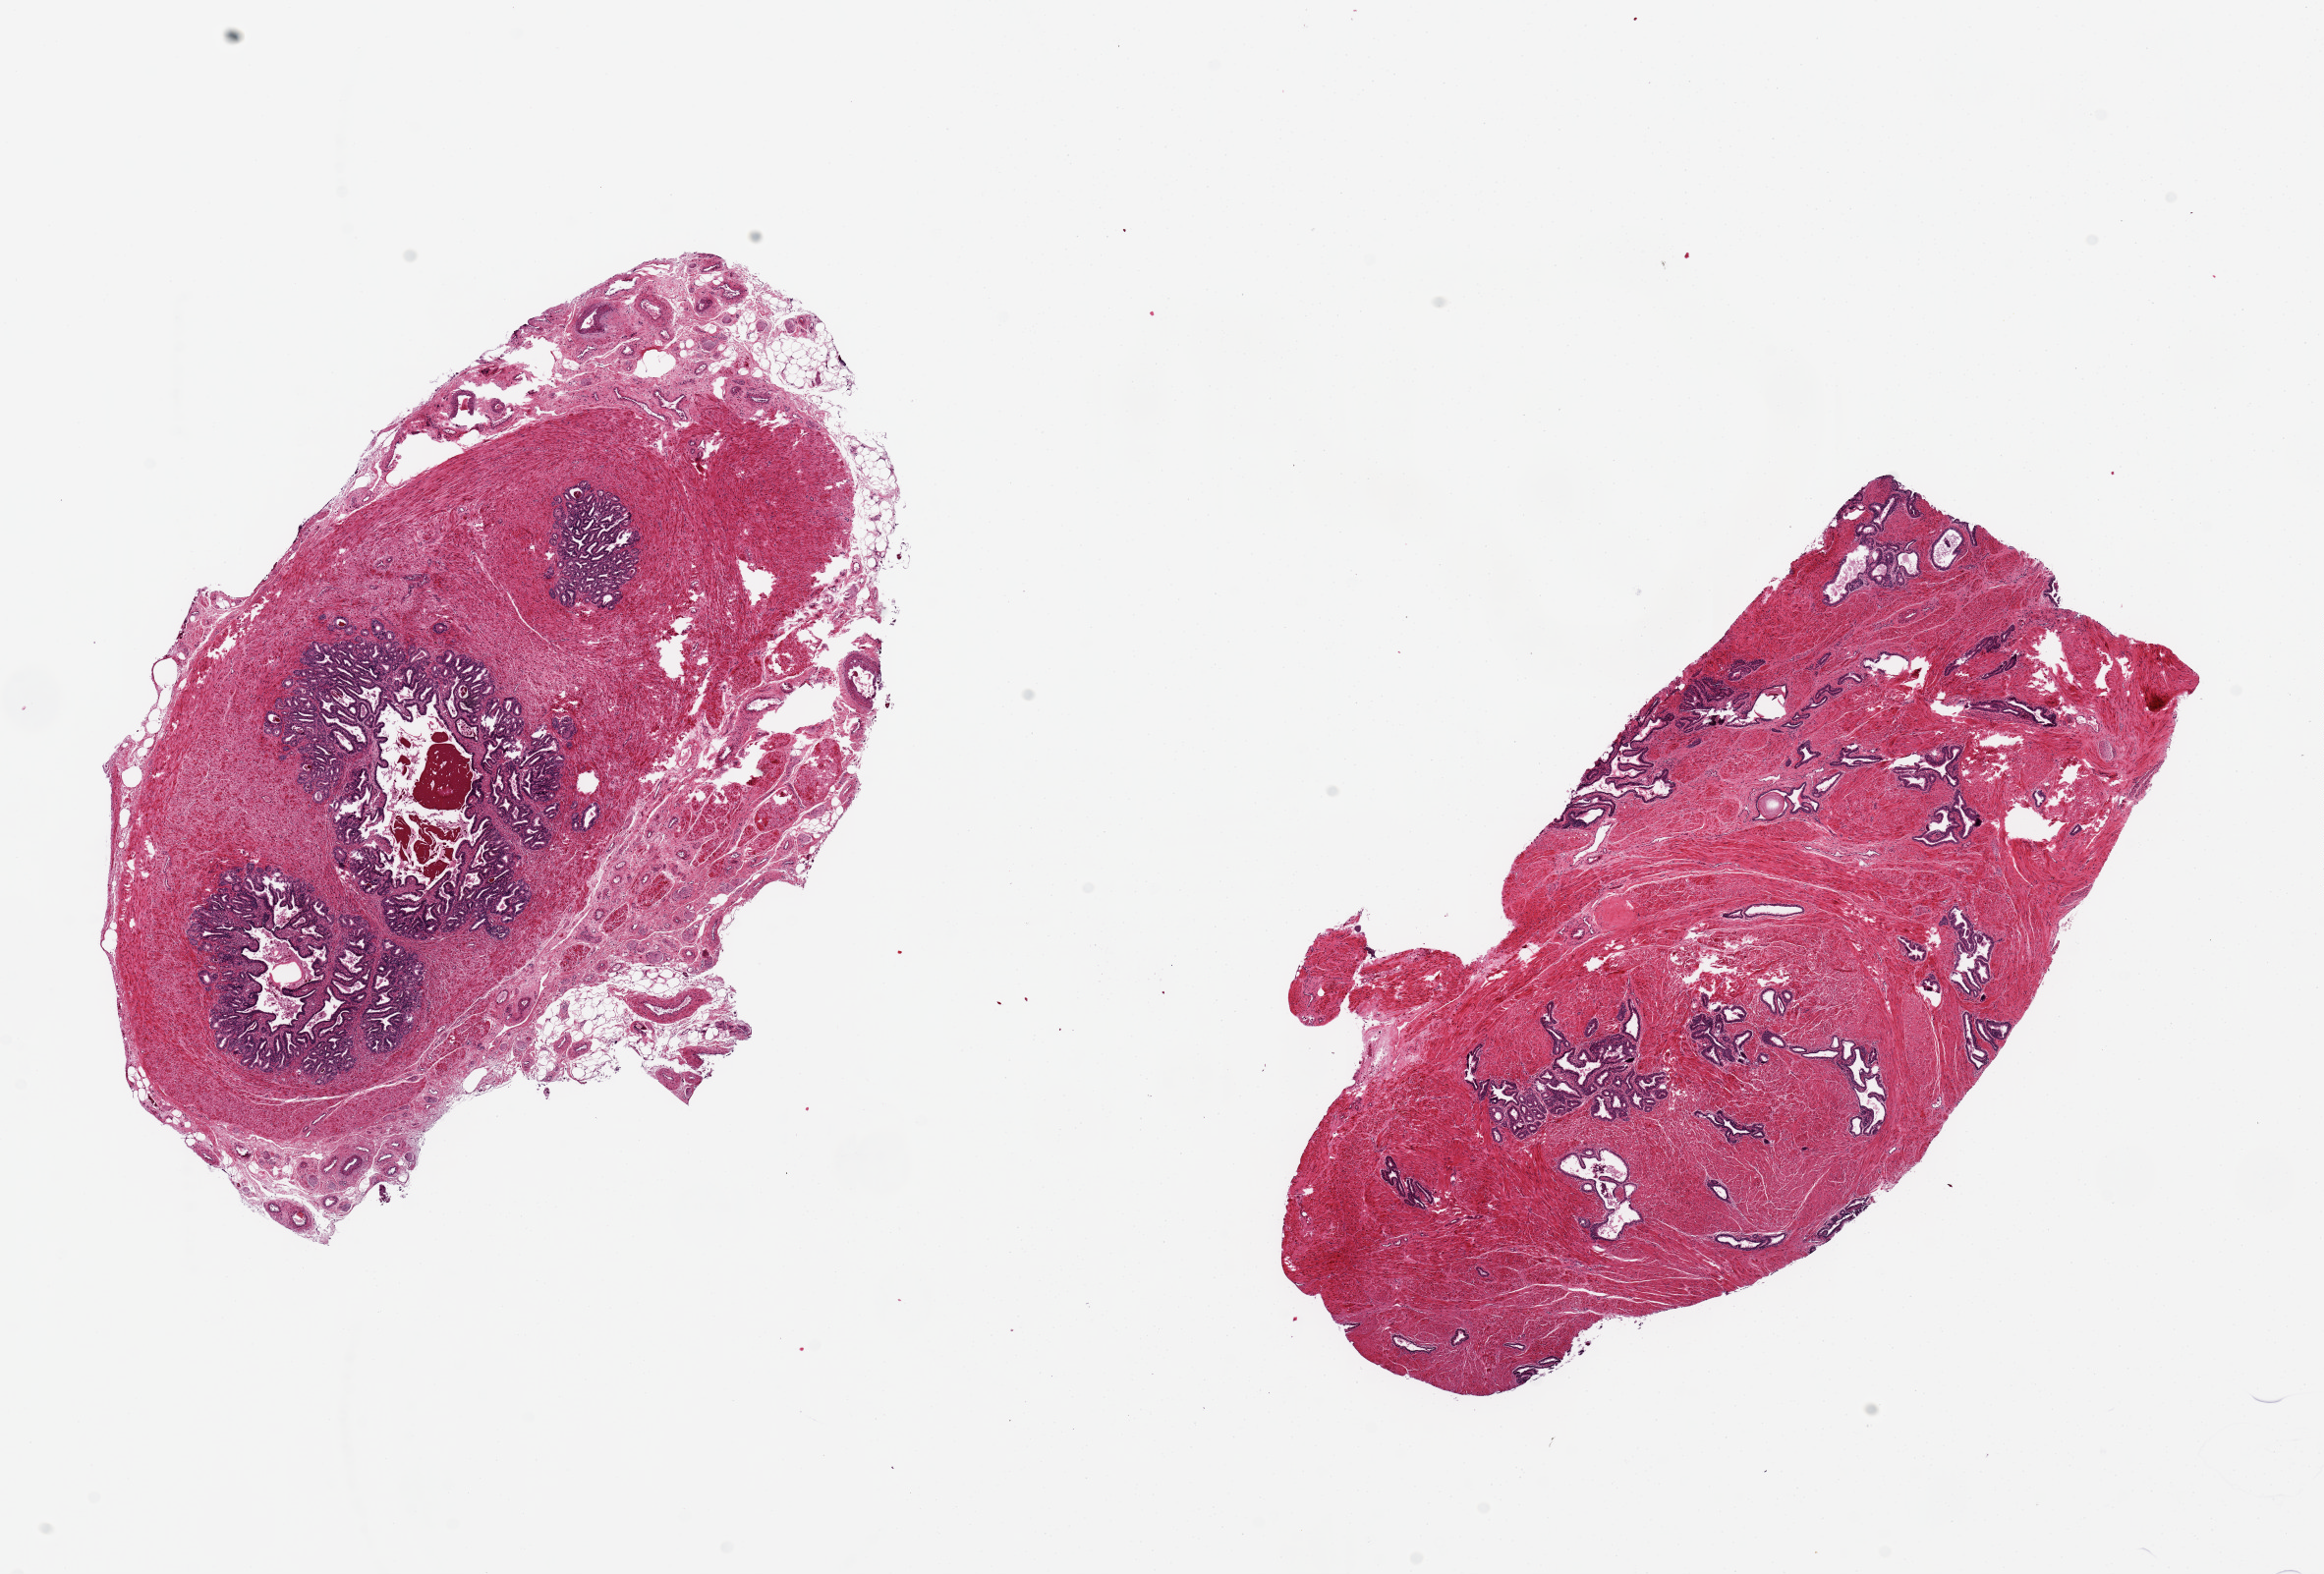
Digitized haematoxylin and eosin-stained section, shown as a low-resolution overview of the whole scanned area (about 18.7 x 12.7 mm), PAXgene-fixed, paraffin-embedded tissue, sampled site (target tissue): prostate, tissue donor sample.
Review note (as recorded): Not prostate, seminal vesicle.